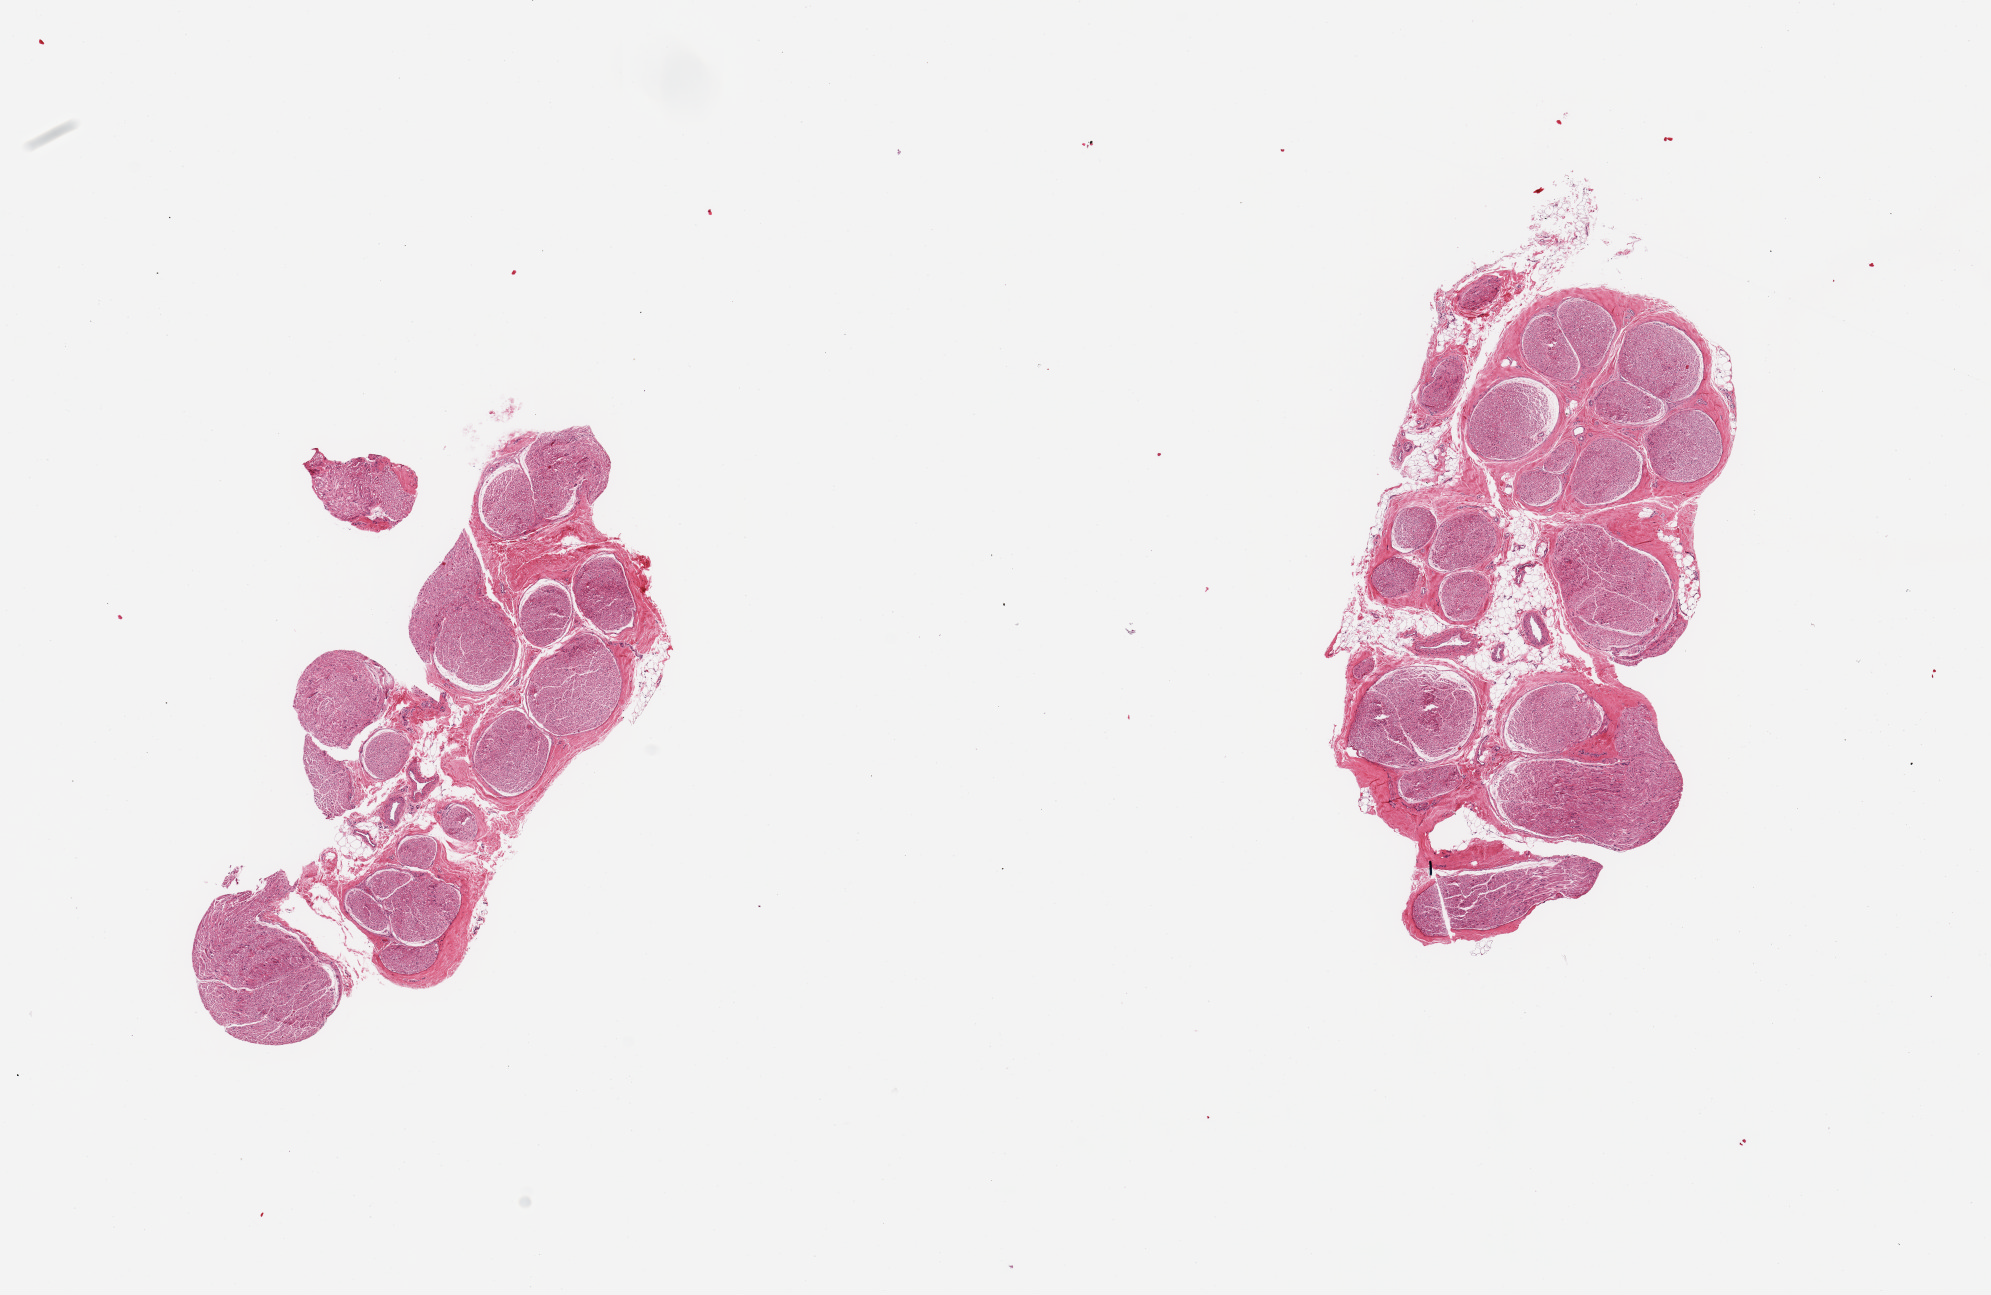
Whole-slide image, haematoxylin and eosin stain, brightfield, a low-resolution overview of the entire scanned area, about 15.8 x 10.2 mm (slide scanned at 20x). PAXgene-fixed, paraffin-embedded tissue. Target tissue: tibial nerve. Tissue donor sample. Donor sex: male.
Review note (as recorded): 2 pieces, no significant adherent fat.